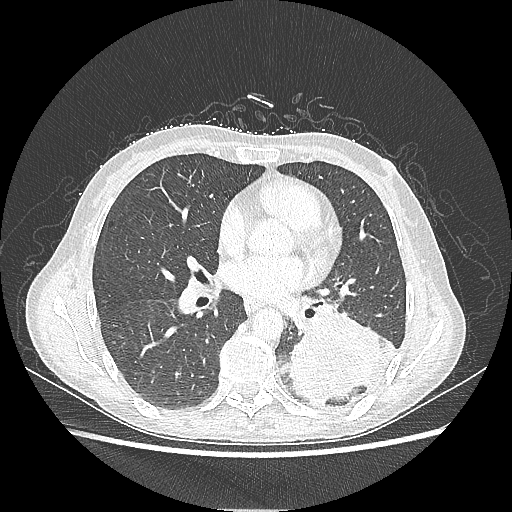
Chest CT, one axial slice; position 109 of 220 along the scan axis; lung window (W 1500 / L -600 HU); 1.25 mm slice thickness; 512 × 512 image matrix, field of view 360 × 360 mm. Patient: female, 53 years. From the clinical record (not read from this slice): clinical TNM (as recorded): T3 N0 M0.
Annotated regions visible in this slice (bounding box drawn by a radiologist):
- lung tumour (recorded histology: adenocarcinoma): box from (x=289, y=306) to (x=396, y=402) px